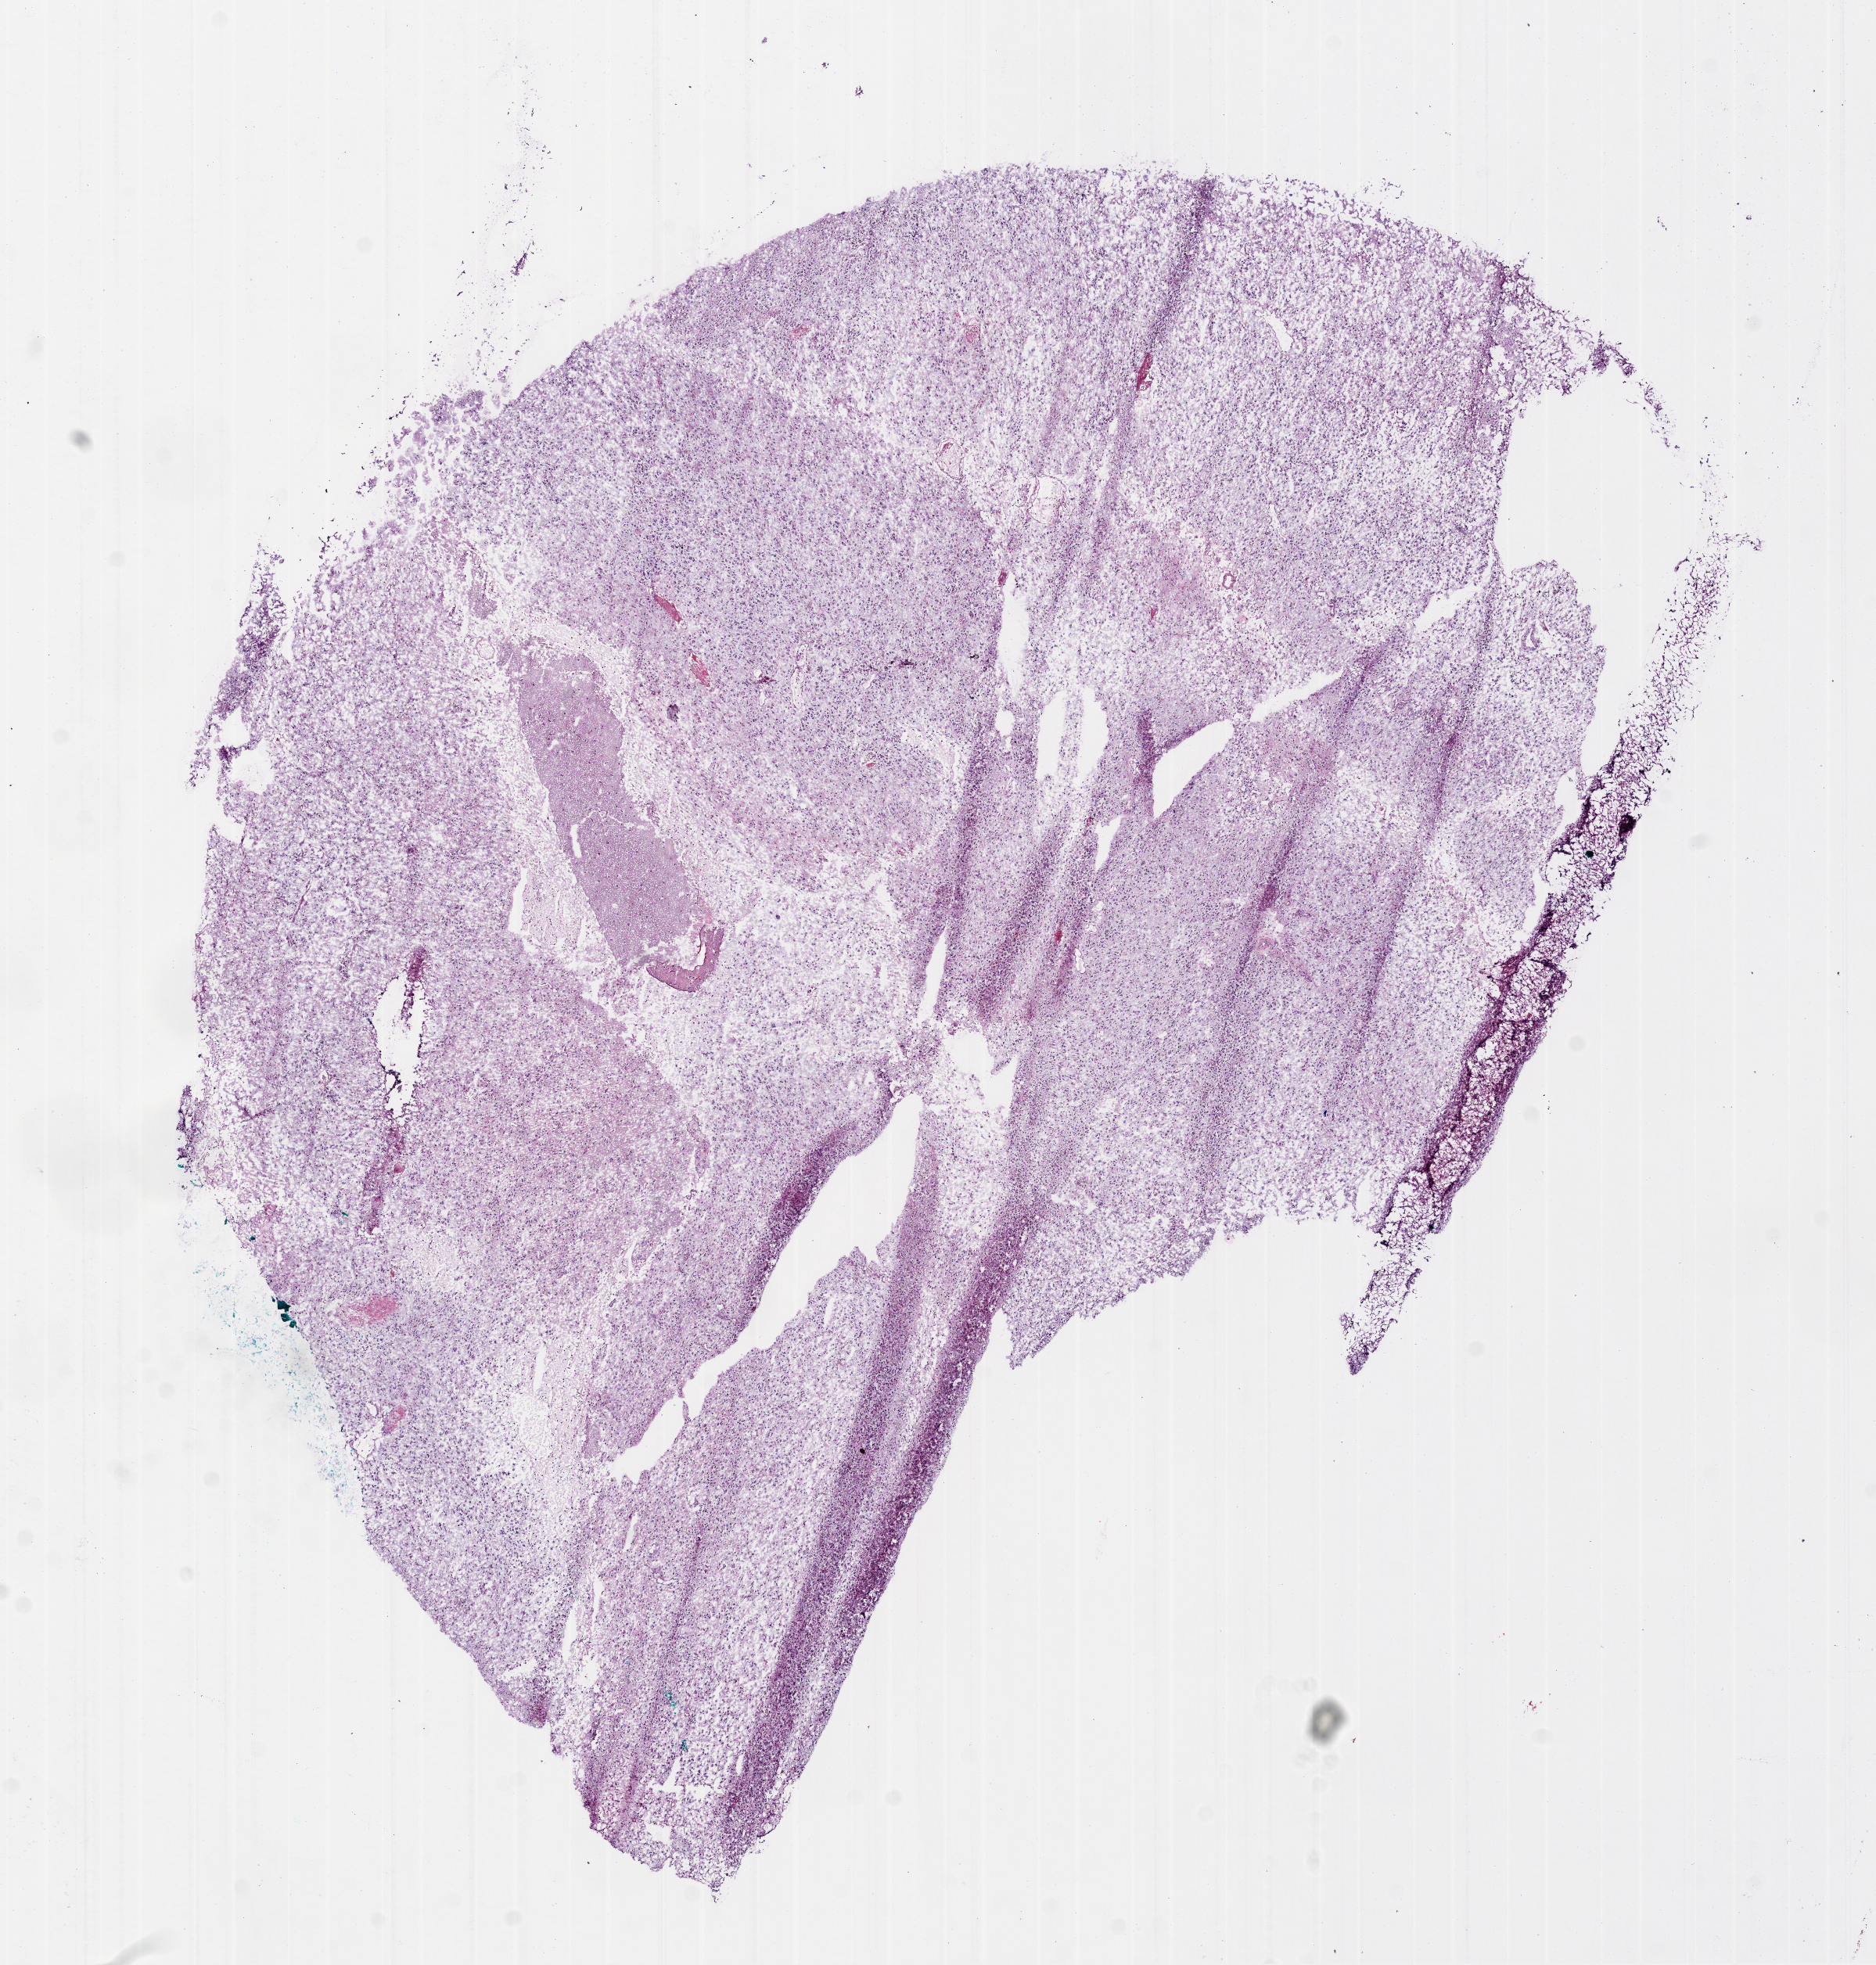
Whole-slide histology image, H&E-stained, a low-resolution overview of the entire scanned area, about 9.7 x 10.1 mm (acquisition: 20x scan), frozen section from the bottom of the tissue portion, primary tumour sample from the brain. Male patient; age at initial diagnosis 63 years. Pathologist review of this section (percent, as recorded): tumour cells 90%, tumour nuclei 90%, normal cells 0%, stromal cells 5%, necrosis 5%.
Histologic diagnosis: Glioblastoma.